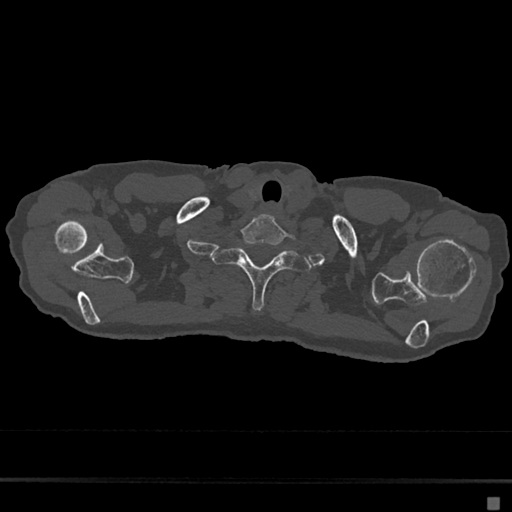
CT including the spine, one axial slice; slice 617 of 797 in the series (ordered by position); bone window (W 1800 / L 400 HU); 512 × 512 image matrix, field of view 360 × 360 mm. Female patient, age 68 years. Case-level facts recorded for this patient, not image findings: primary cancer: renal.
Annotated regions visible in this slice (semi-automatically segmented with operator editing):
- T1 vertebra: box from (x=212, y=239) to (x=312, y=310) px